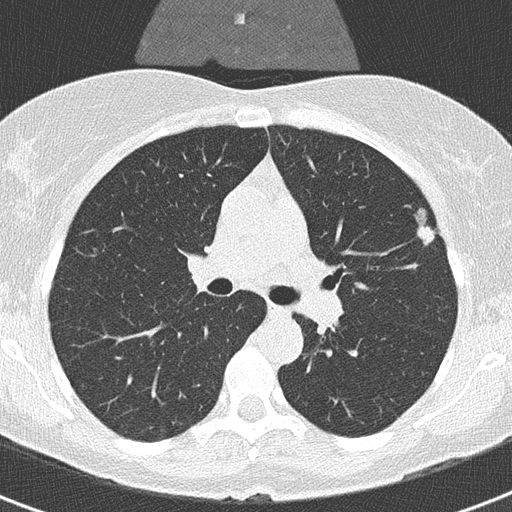
Chest CT (low-dose screening protocol), one axial image; second annual screen; lung window (W 1500 / L -600 HU); 2 mm slice thickness; lung (sharp) reconstruction kernel (B50f); 120 kVp; slice 113 of 320 in the series. Female, age 56 years at enrolment. Former smoker at enrolment.
Expert-annotated lung lesion, bounding box (x1, y1, x2, y2) in pixels: (405, 201, 454, 255). The exam's reader record, not a measurement of the box and not confirmed to be the same lesion: non-calcified nodule or mass ≥4 mm, left upper lobe, 20 × 9 mm, smooth margins, soft tissue attenuation, pre-existing on the prior screen: yes; interval growth: yes. Official screen result: positive, other. Later outcome: lung cancer diagnosed 55 days after this screen — adenocarcinoma, NOS, left upper lobe, moderately differentiated (G2), stage IA (AJCC 6th edition), 11 mm at pathology.